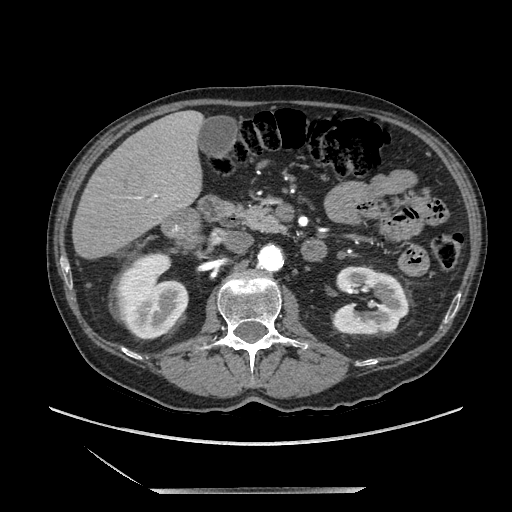
Contrast-enhanced abdominal CT, one axial slice. Soft-tissue window (W 400 / L 40 HU). 512 × 512 image matrix, field of view 420 × 420 mm. Male patient. Case-level facts recorded for this patient, not image findings: diagnosis: adrenocortical carcinoma; tumour side: right adrenal; tumour size at pathology: 16 cm; Ki-67 index: 17 %; stage (as recorded): 3.
Annotated regions visible in this slice (semi-automatic segmentation, software-assisted and operator-edited):
- mass: bounding box (x1, y1, x2, y2) in pixels: (167, 211, 201, 249)